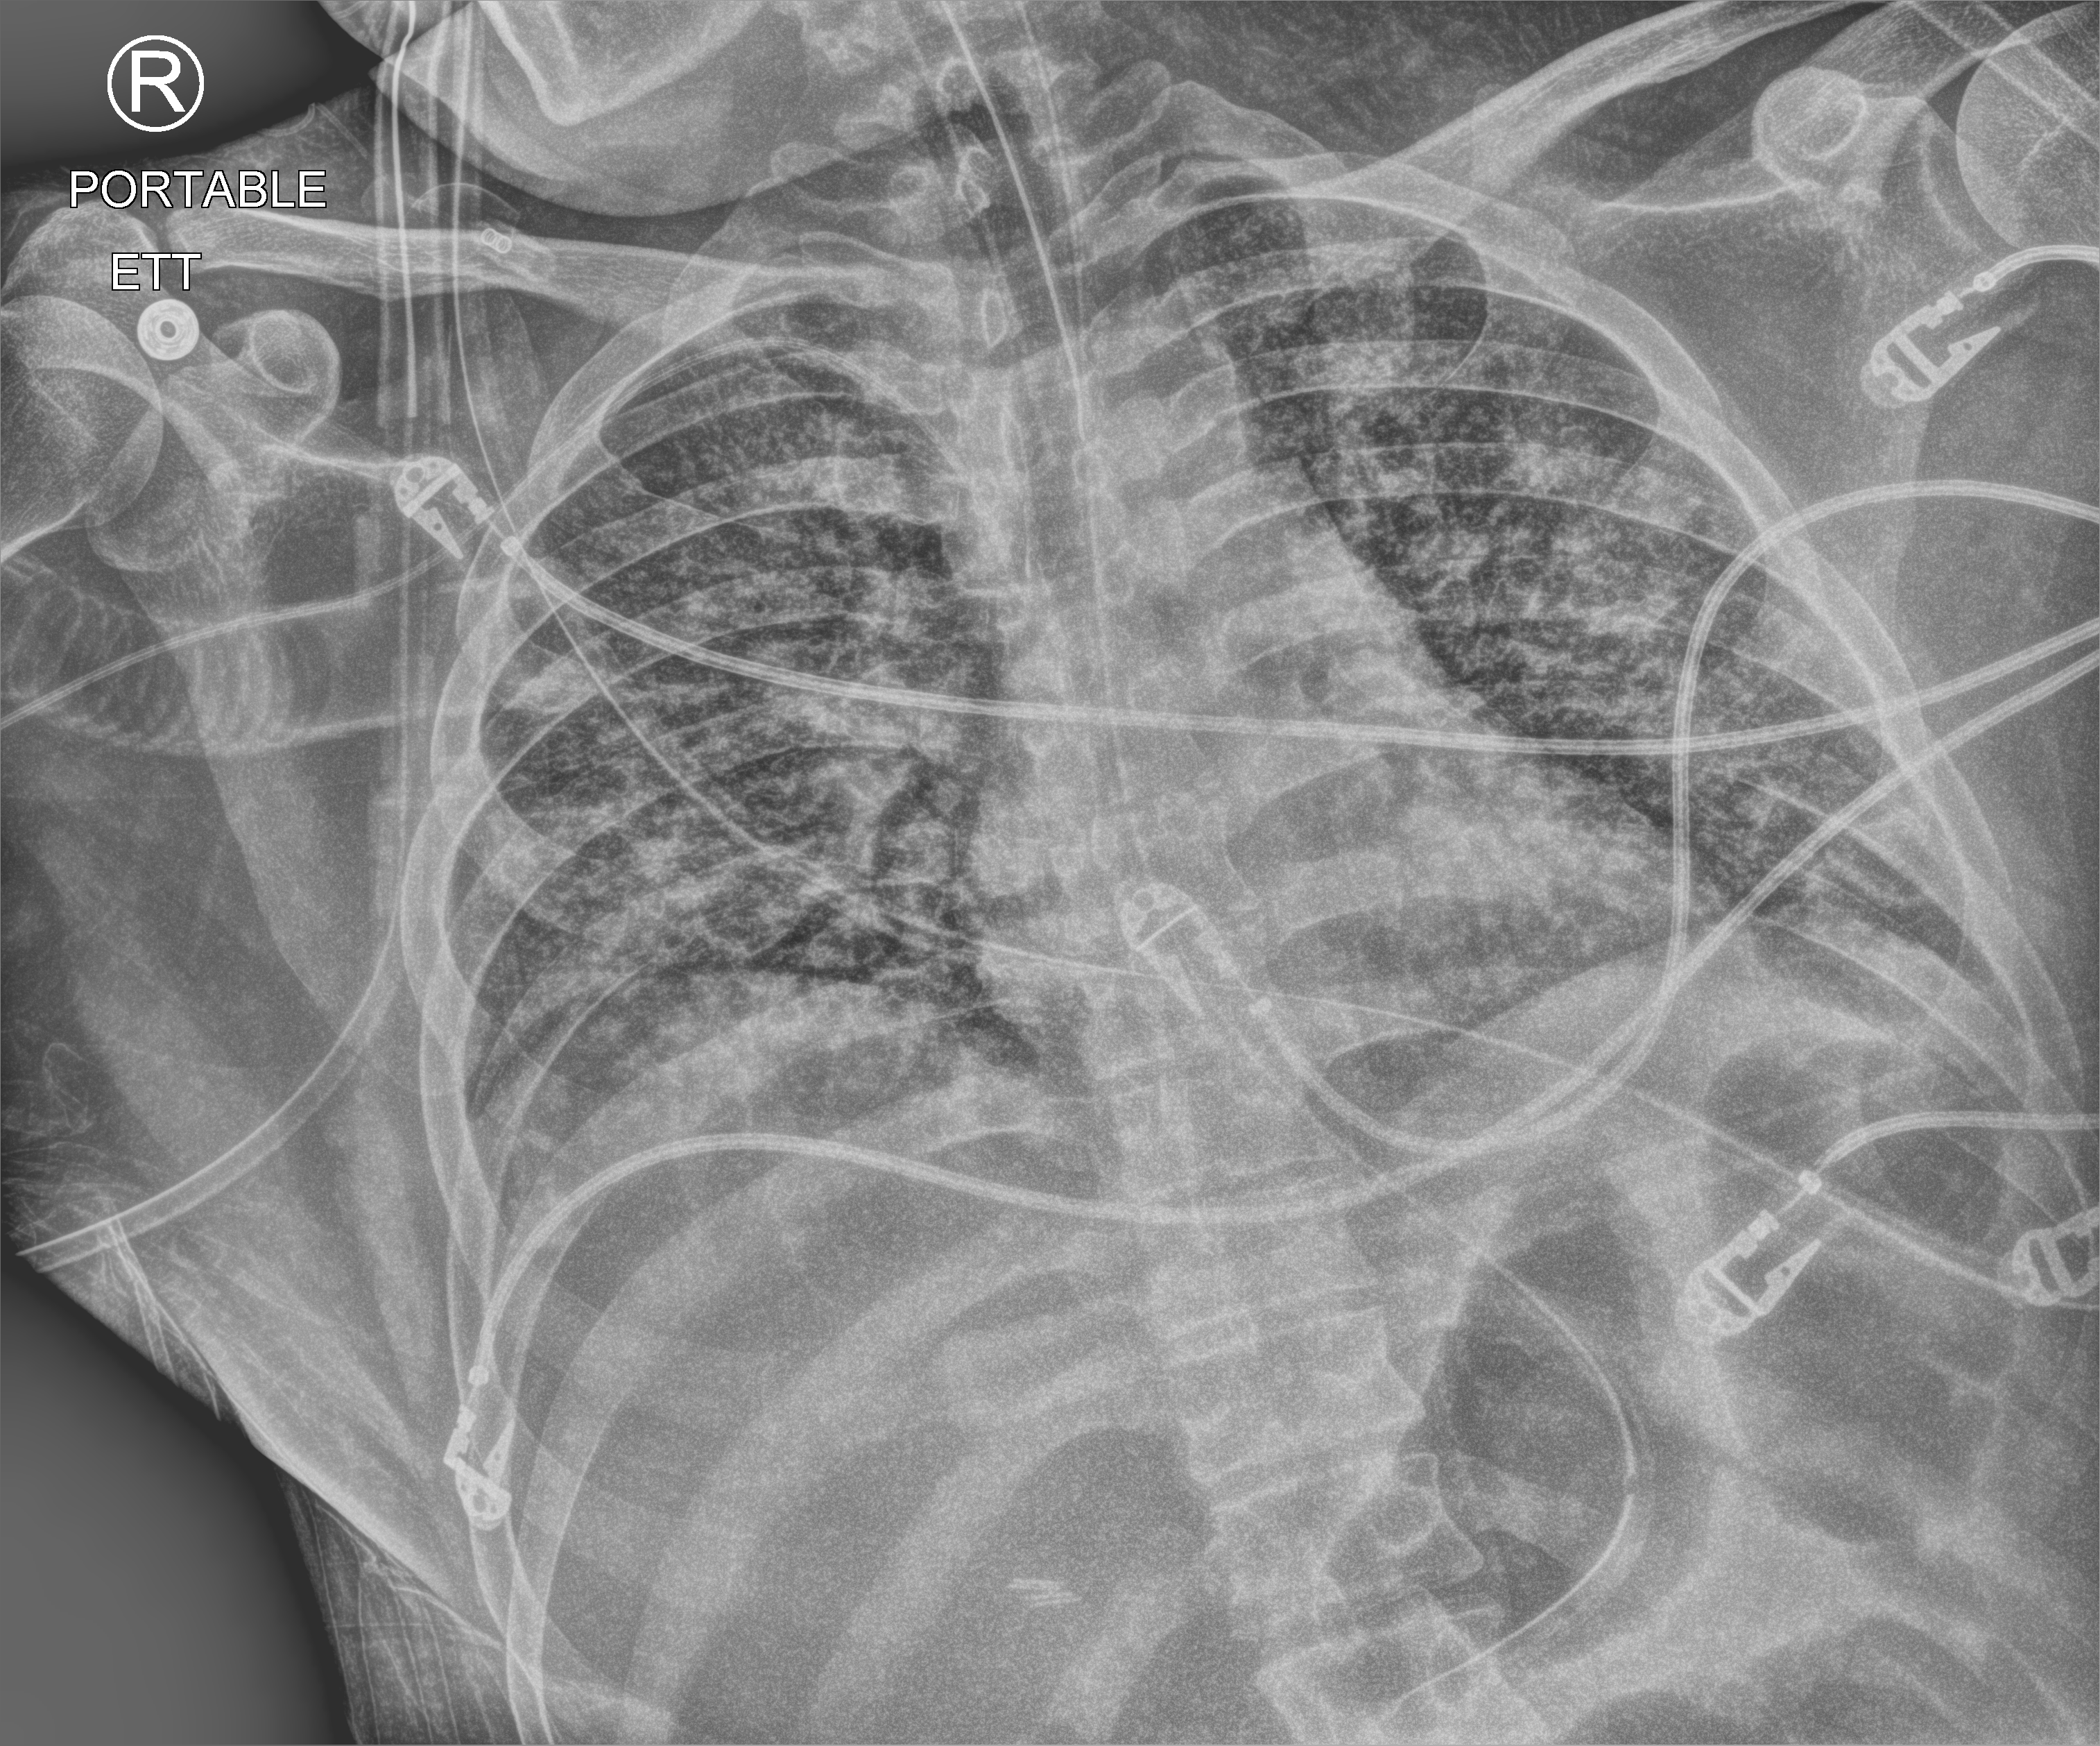
Bedside chest radiograph (computed radiography); anteroposterior (AP) projection. Male patient hospitalised with COVID-19, age 18–59 years.
From the hospital-stay record, not from the radiograph (when in the stay this image was taken is not recorded):
- mechanically ventilated during this hospital stay: yes